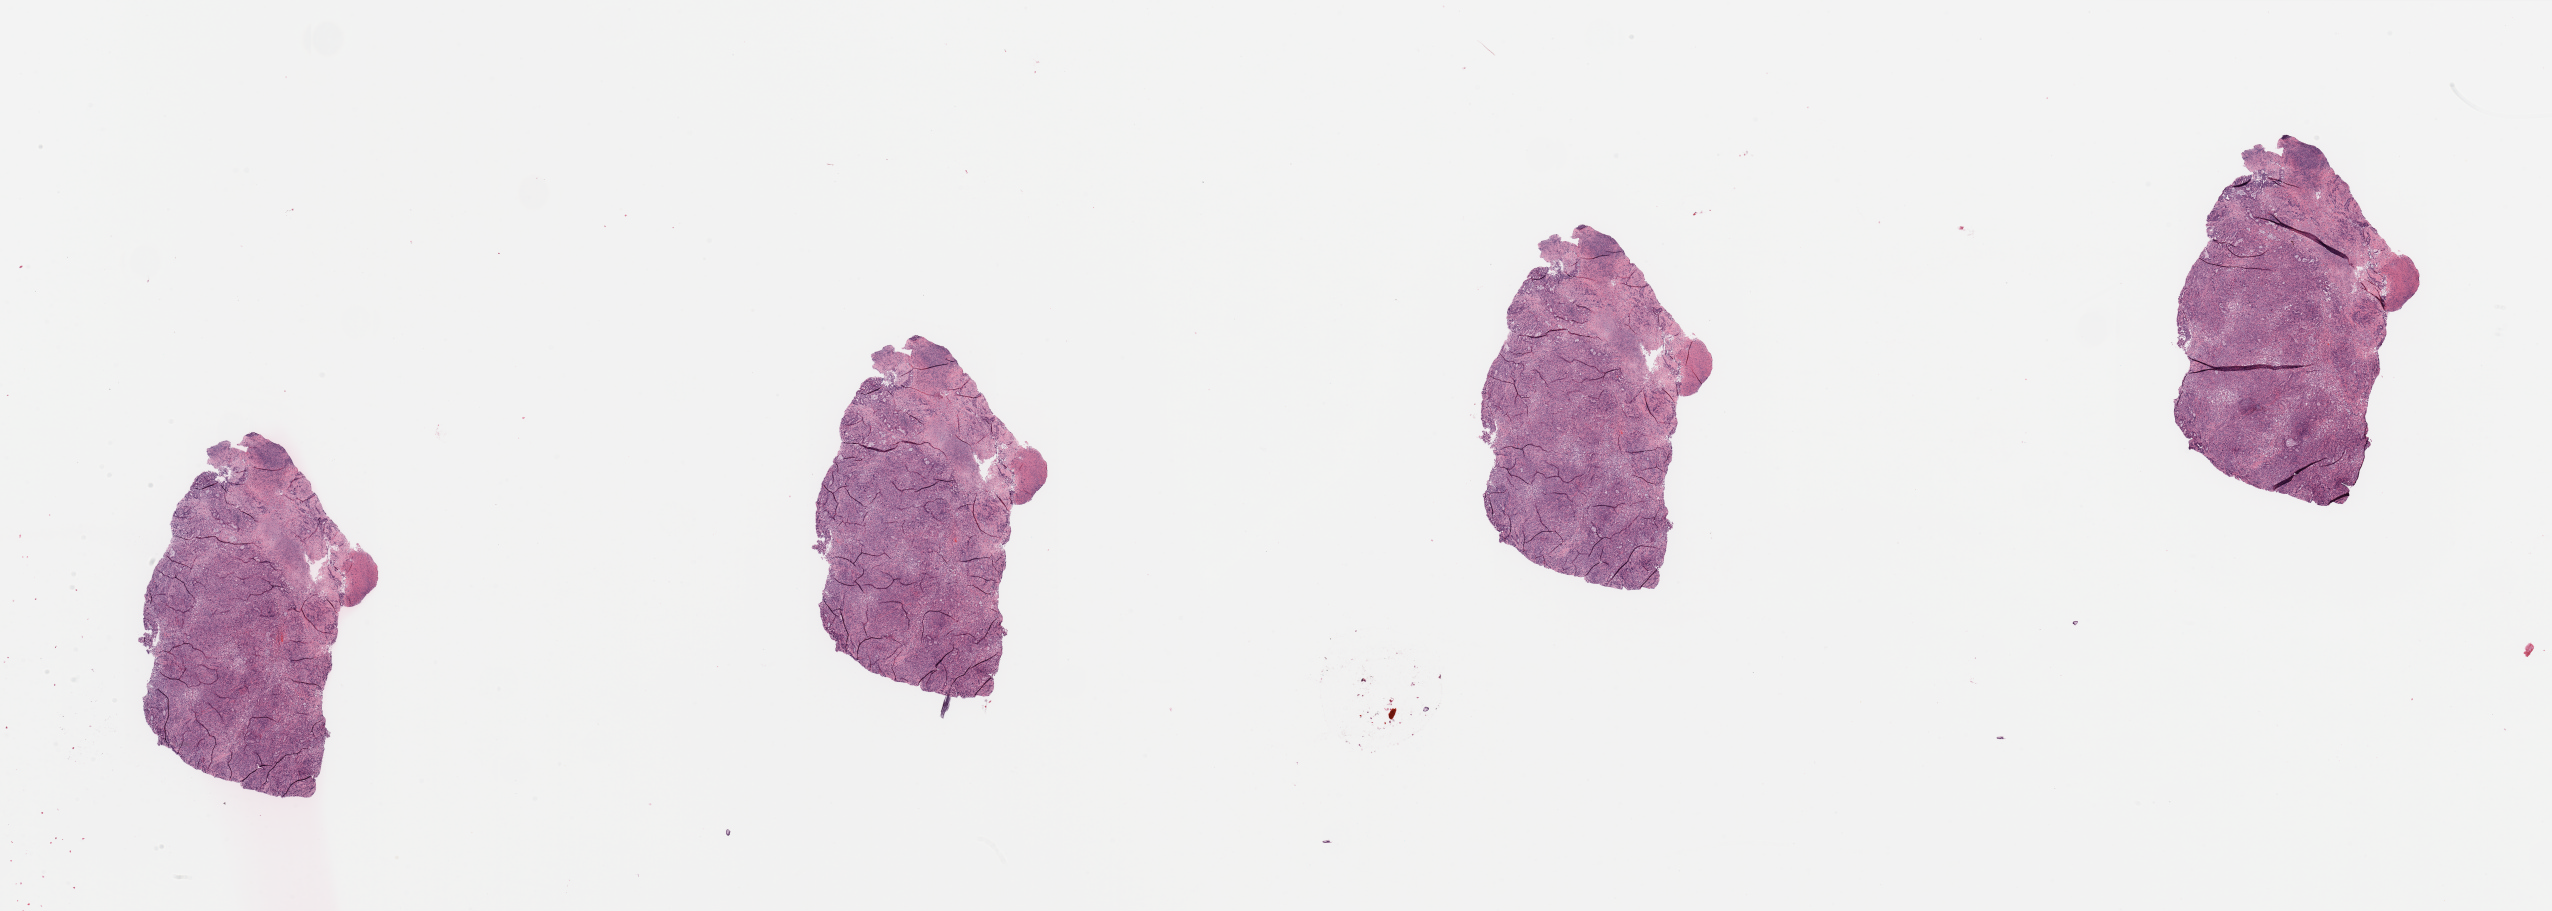
Whole-slide histology image, H&E — shown as a low-resolution overview of the whole scanned area (about 40.4 x 14.4 mm), tumour tissue sample, sampled site: pancreas. 52-year-old female patient. Composition of this section per pathologist review: tumour nuclei 90%, necrosis 15%.
Histologic diagnosis: Infiltrating duct carcinoma, NOS.